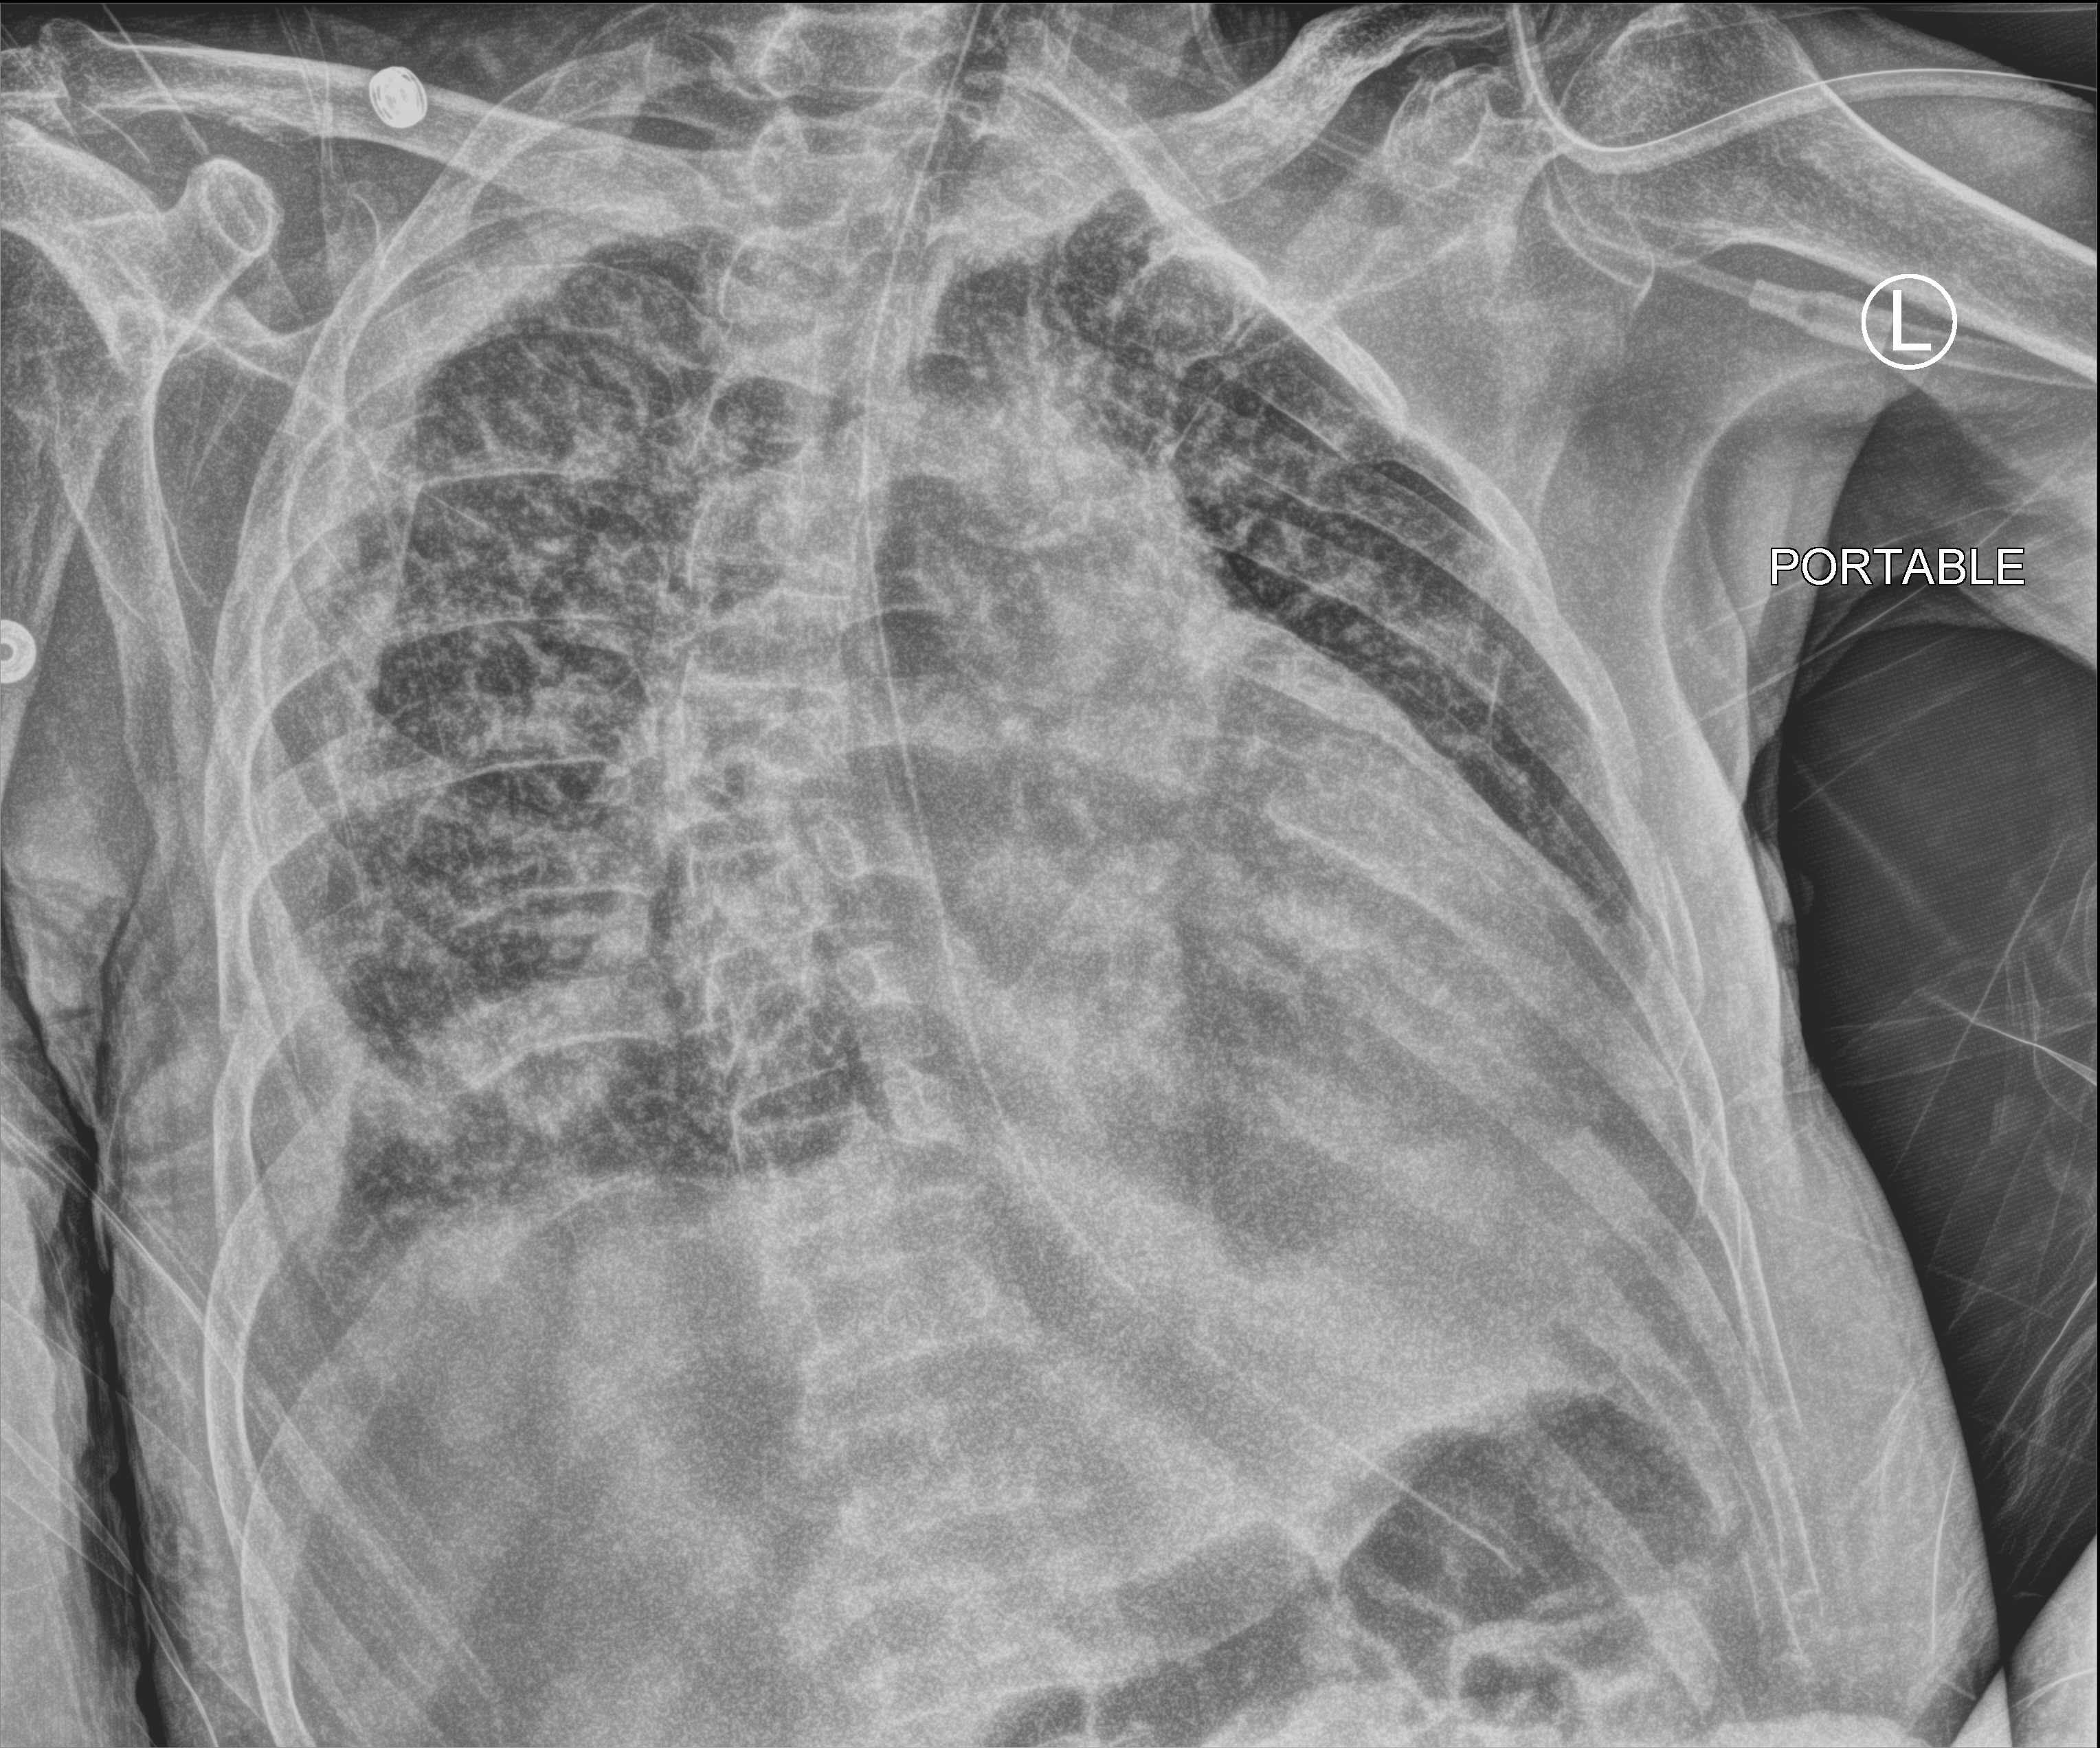
Bedside chest radiograph (computed radiography), anteroposterior (AP) projection. Male patient hospitalised with COVID-19, age 75–90 years.
Hospital-stay facts (about this admission, not read from this image; timing relative to this image not recorded): chronic kidney disease (admission record): no; mechanically ventilated during this hospital stay: no; length of hospital stay: 14 days.